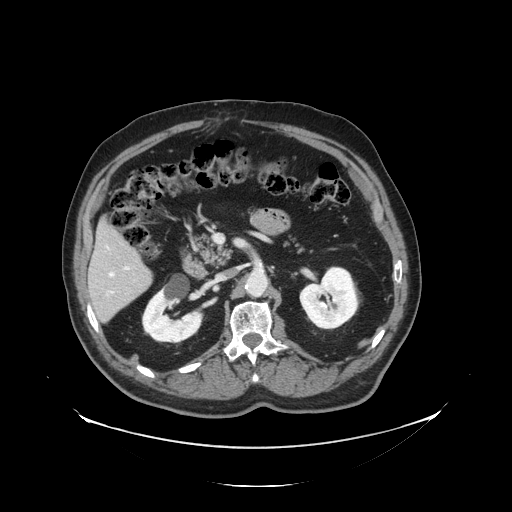
Contrast-enhanced abdominal CT, one axial slice. Position 63 of 138 along the scan axis. Reconstruction kernel STANDARD. 120 kVp. Intravenous contrast given. Soft-tissue window (W 400 / L 40 HU). 512 × 512 image matrix. Male patient, age 77 years. From the clinical record (not read from this slice): diagnosis: colorectal cancer liver metastases, imaged before liver resection; multiple liver metastases: no; largest metastasis: 1.5 cm.
Outlined on this slice (expert manual segmentation):
- liver: bounding box <90,223,152,322> (left, top, right, bottom; pixels)
- planned liver remnant (the part of the liver to remain after resection): <90,223,145,286>
- portal vein (with intrahepatic branches): <125,267,129,270>